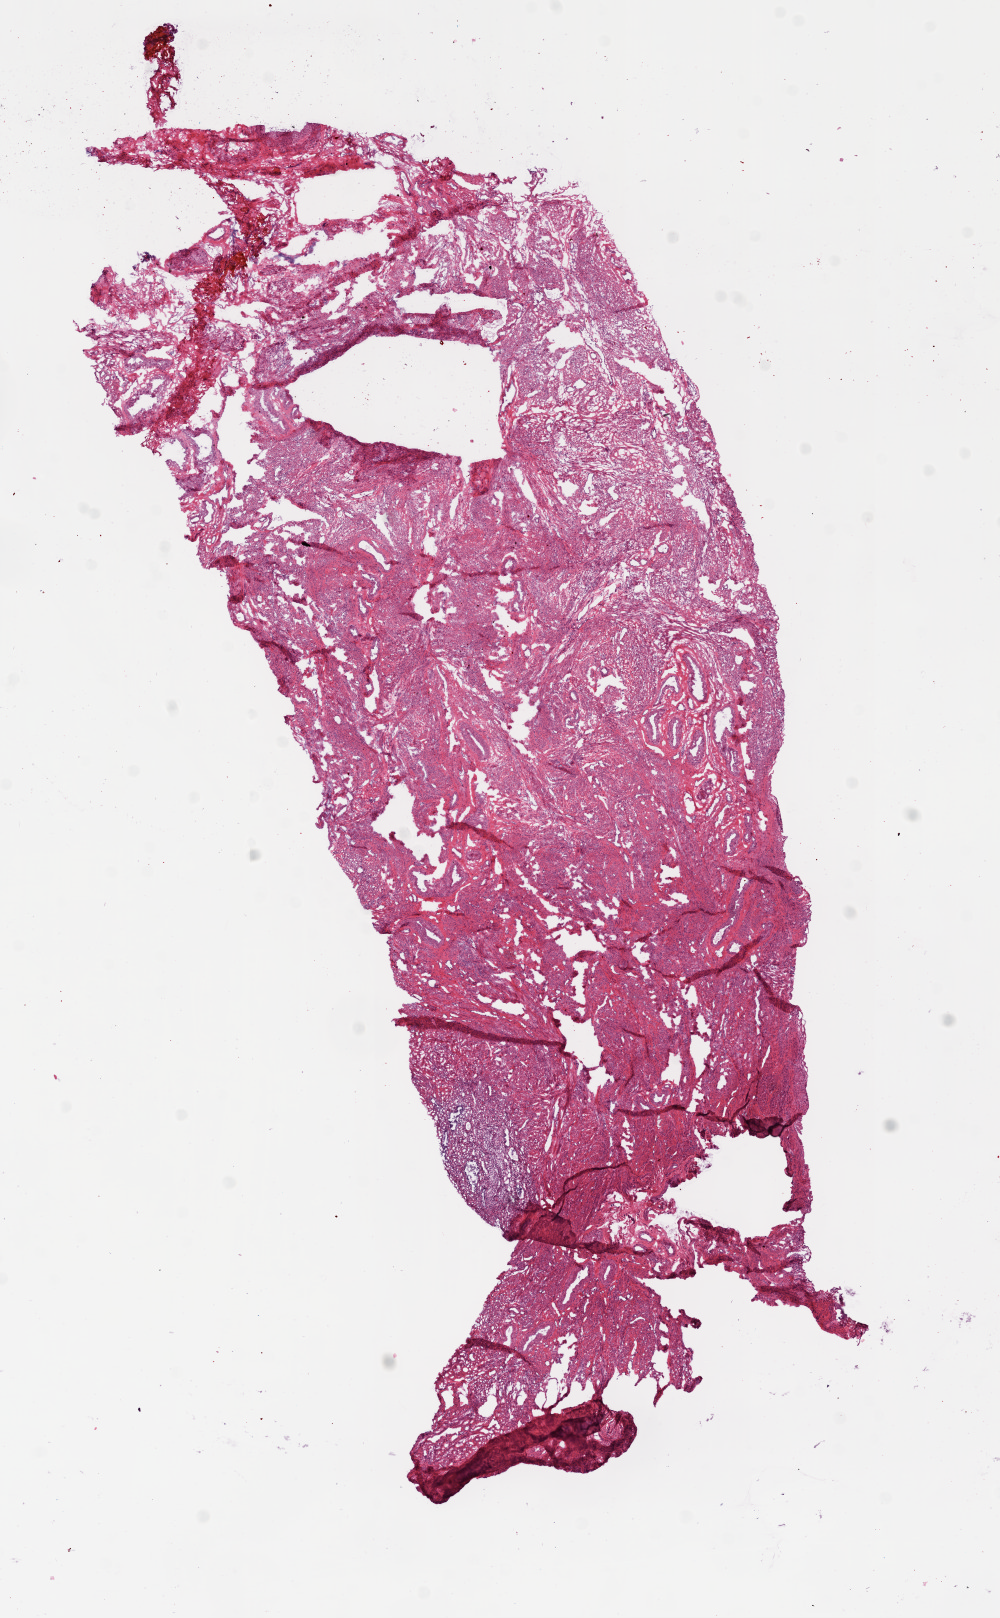
Digitized Hematoxylin and eosin (H&E) stained tissue section (whole slide) — low-resolution overview of the scanned area, about 8.0 x 13.0 mm (from a 20x scan). Frozen section from the bottom of the tissue portion. Sample: solid tissue normal (non-tumour tissue), ovary. Patient: female, age at initial diagnosis 52 years.
This section: solid tissue normal sample (biorepository sample class). Patient diagnosis: Serous cystadenocarcinoma, NOS.